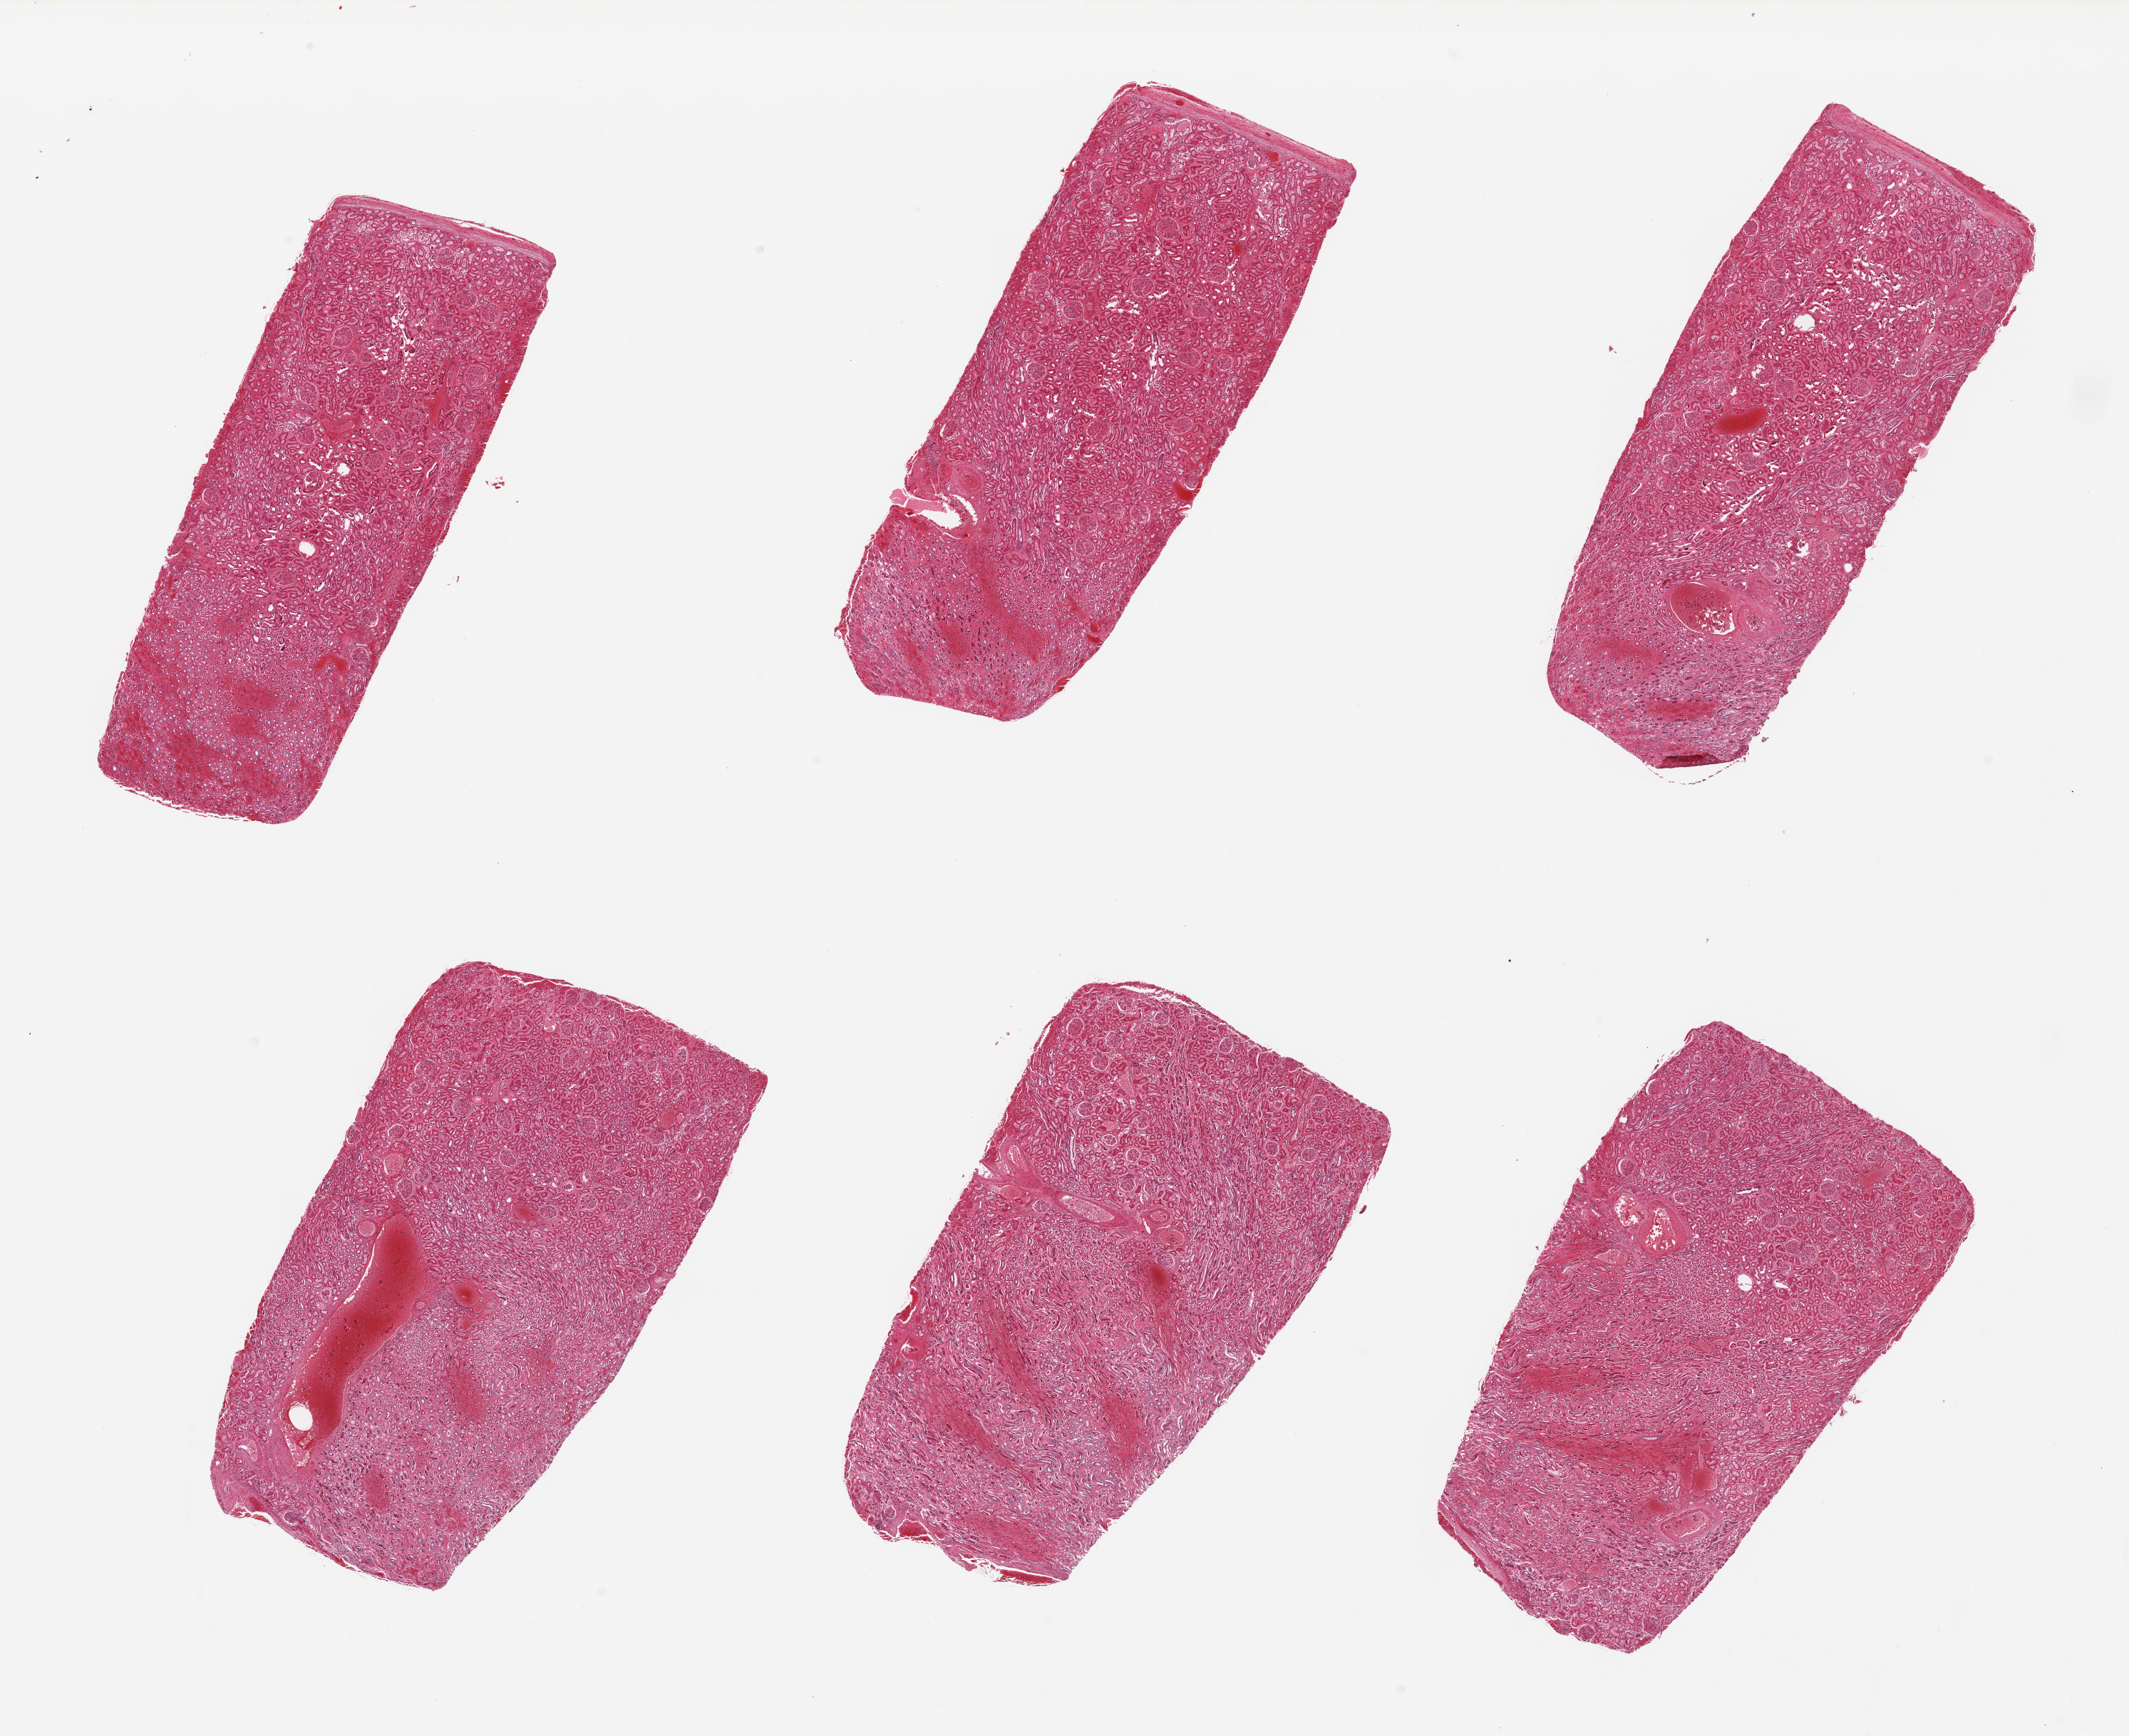
Whole-slide image, H&E stain, a low-resolution overview of the entire scanned area, about 23.6 x 19.3 mm; PAXgene-fixed, paraffin-embedded tissue; target tissue: renal cortex; donor tissue sample. Donor: female.
Reviewer comment on this tissue sample: 6 pieces, glomeruli noted in all, modeately autolyzed.